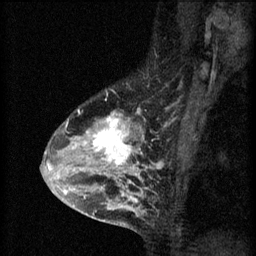
Breast MRI (dynamic contrast-enhanced), one sagittal slice. Slice 41 of 60 in the series (ordered by position). 3 images stored at this slice position (order not interpretable as contrast timing). 1.5 T. TE 4.2 ms, TR 8.2 ms. 2 mm slice thickness. 256 × 256 image matrix, field of view 180 × 180 mm. Patient: female, 45 years.
Annotated regions visible in this slice (semi-automatic segmentation, software-assisted and operator-edited):
- analysis volume of interest (the breast-tissue region the enhancement analysis was run in; not a lesion): bounding box [x1, y1, x2, y2] px = [54, 104, 159, 217]
- tumour enhancement mask (voxels above the 70 % enhancement threshold inside the analysis volume of interest): [54, 108, 147, 217]